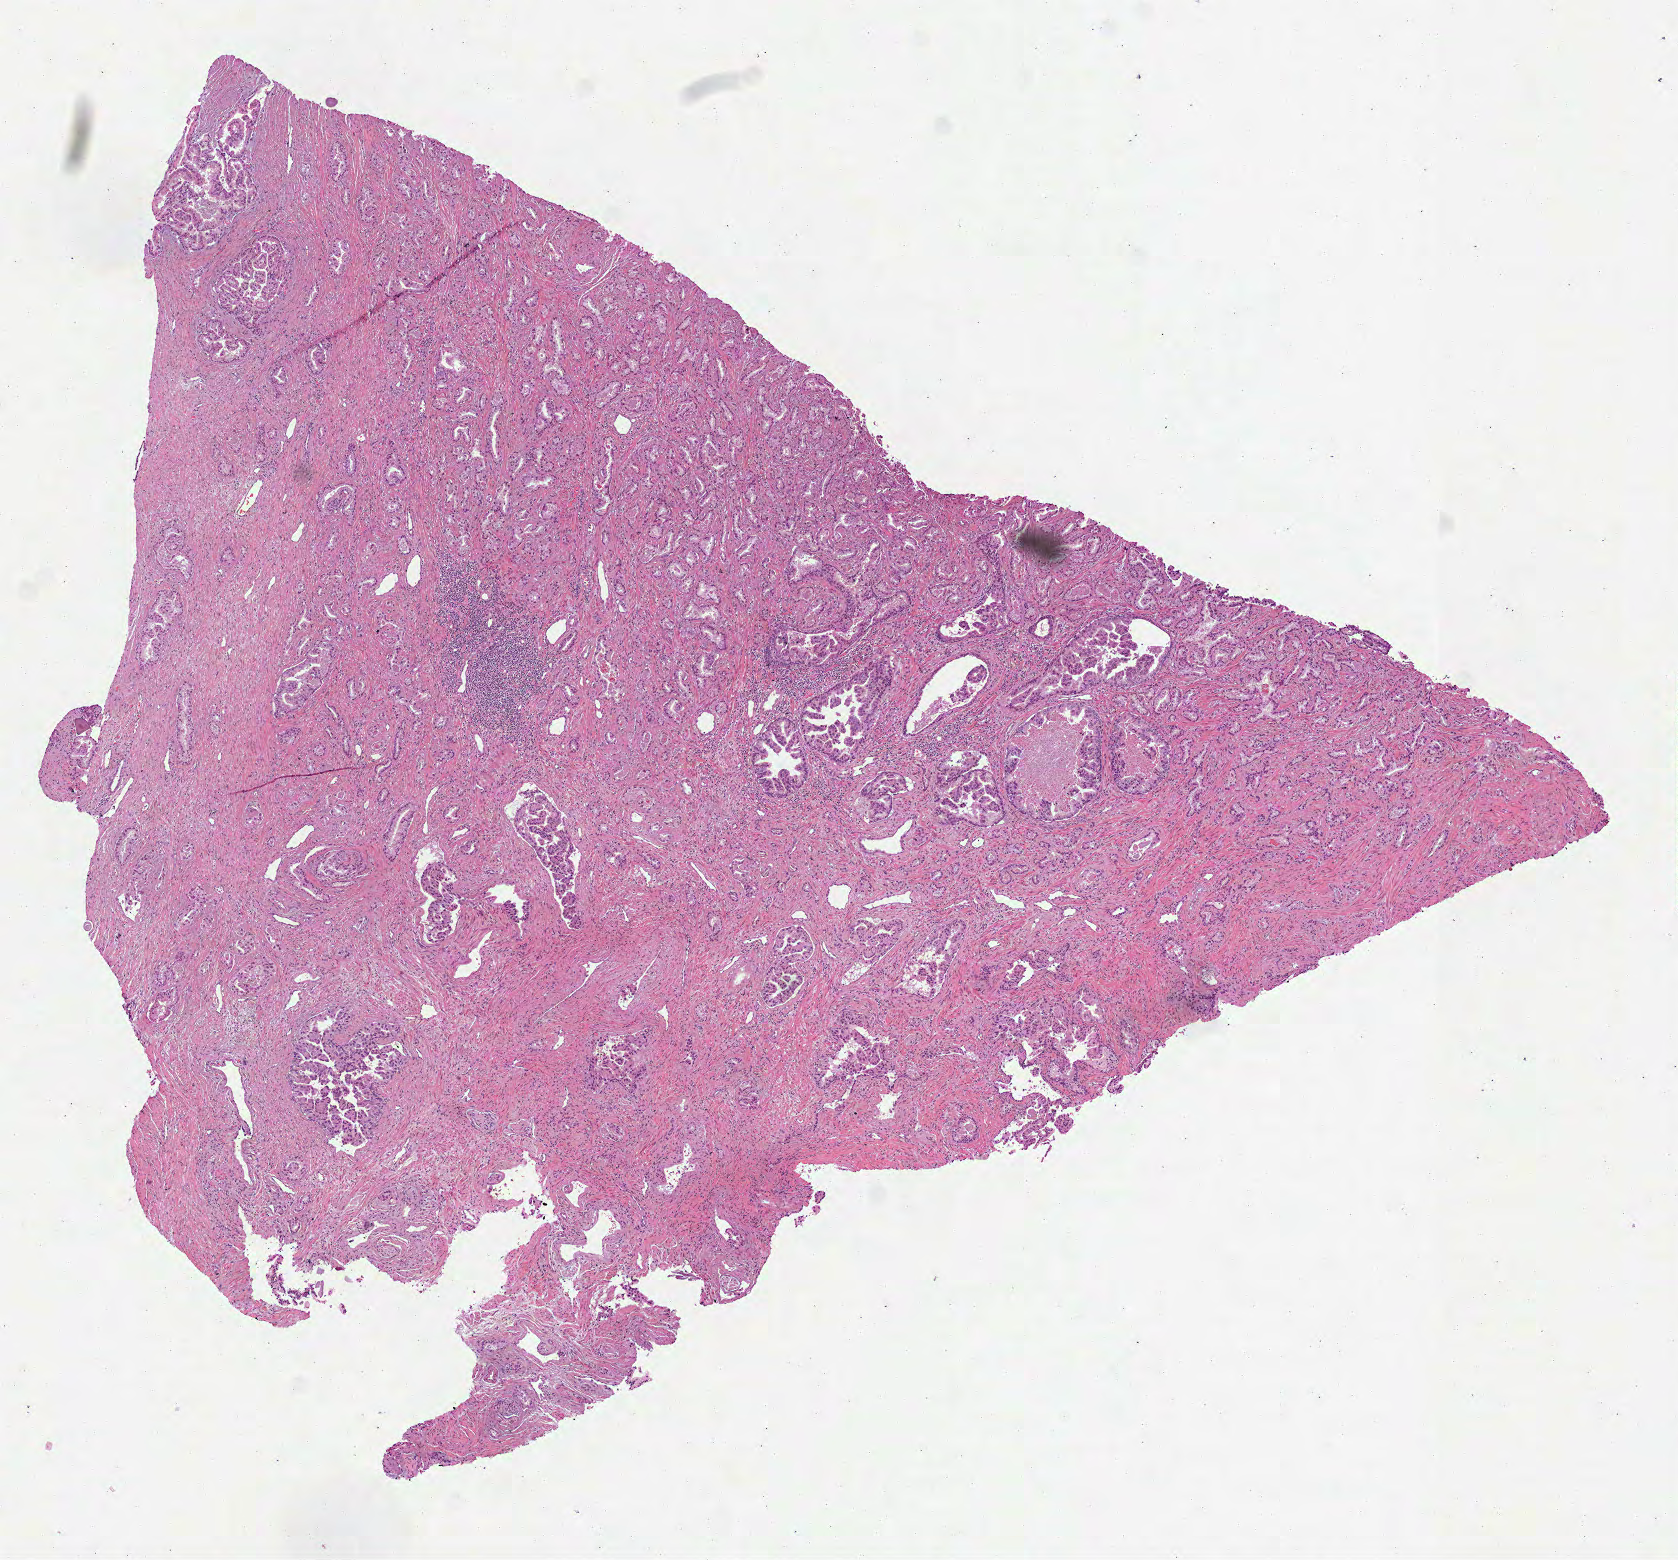
Digitized H&E tissue section (whole slide) — a low-resolution overview of the entire scanned area, about 6.8 x 6.3 mm (slide scanned at 40x); formalin-fixed paraffin-embedded (FFPE) diagnostic section; prostate, primary tumour sample. Male, age 52 years at initial diagnosis. Gleason score: 7 (4+3).
Pathologic diagnosis: Adenocarcinoma, NOS (prostate gland). Laterality: bilateral.